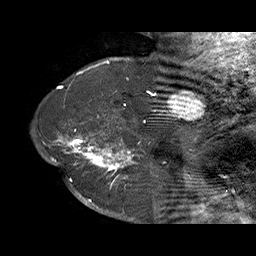
Breast MRI (dynamic contrast-enhanced), one sagittal slice; slice 53 of 70 in the series (ordered by position); dynamic contrast-enhanced series, time point 2 of 6 at this slice position (early post-contrast); 1.5 T; TE 4.5 ms, TR 32.4 ms; 3 mm slice thickness; 256 × 256 image matrix, field of view 180 × 180 mm. Female patient. Case-level facts recorded for this patient, not image findings: setting: breast cancer imaged before/during neoadjuvant chemotherapy; receptor status: HR-positive, HER2-negative.
Outlined on this slice (semi-automatically segmented with operator editing):
- analysis volume of interest (the breast-tissue region the enhancement analysis was run in; not a lesion): box from (x=71, y=128) to (x=159, y=202) px
- tumour enhancement mask (voxels above the 100 % enhancement threshold inside the analysis volume of interest): (x=71, y=129)–(x=150, y=202)